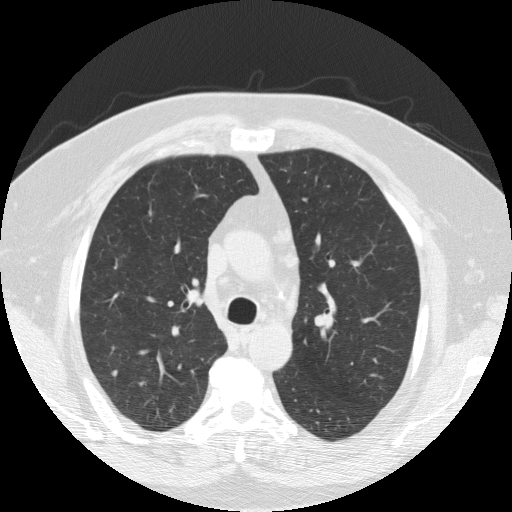
Low-dose screening chest CT, axial slice. Second screening round (one year after baseline). Lung window (W 1500 / L -600 HU). 512 × 512 image matrix. Male participant, aged 60 years at enrolment. Current smoker at enrolment.
Expert reader's lesion annotation, bounding box [x1, y1, x2, y2] px = [313, 306, 340, 336]. No non-calcified nodule or mass ≥4 mm was recorded by the screening reader at this exam. Participant outcome: lung cancer diagnosed 425 days after this screen — squamous cell carcinoma, NOS, right upper lobe, 27 mm at pathology.